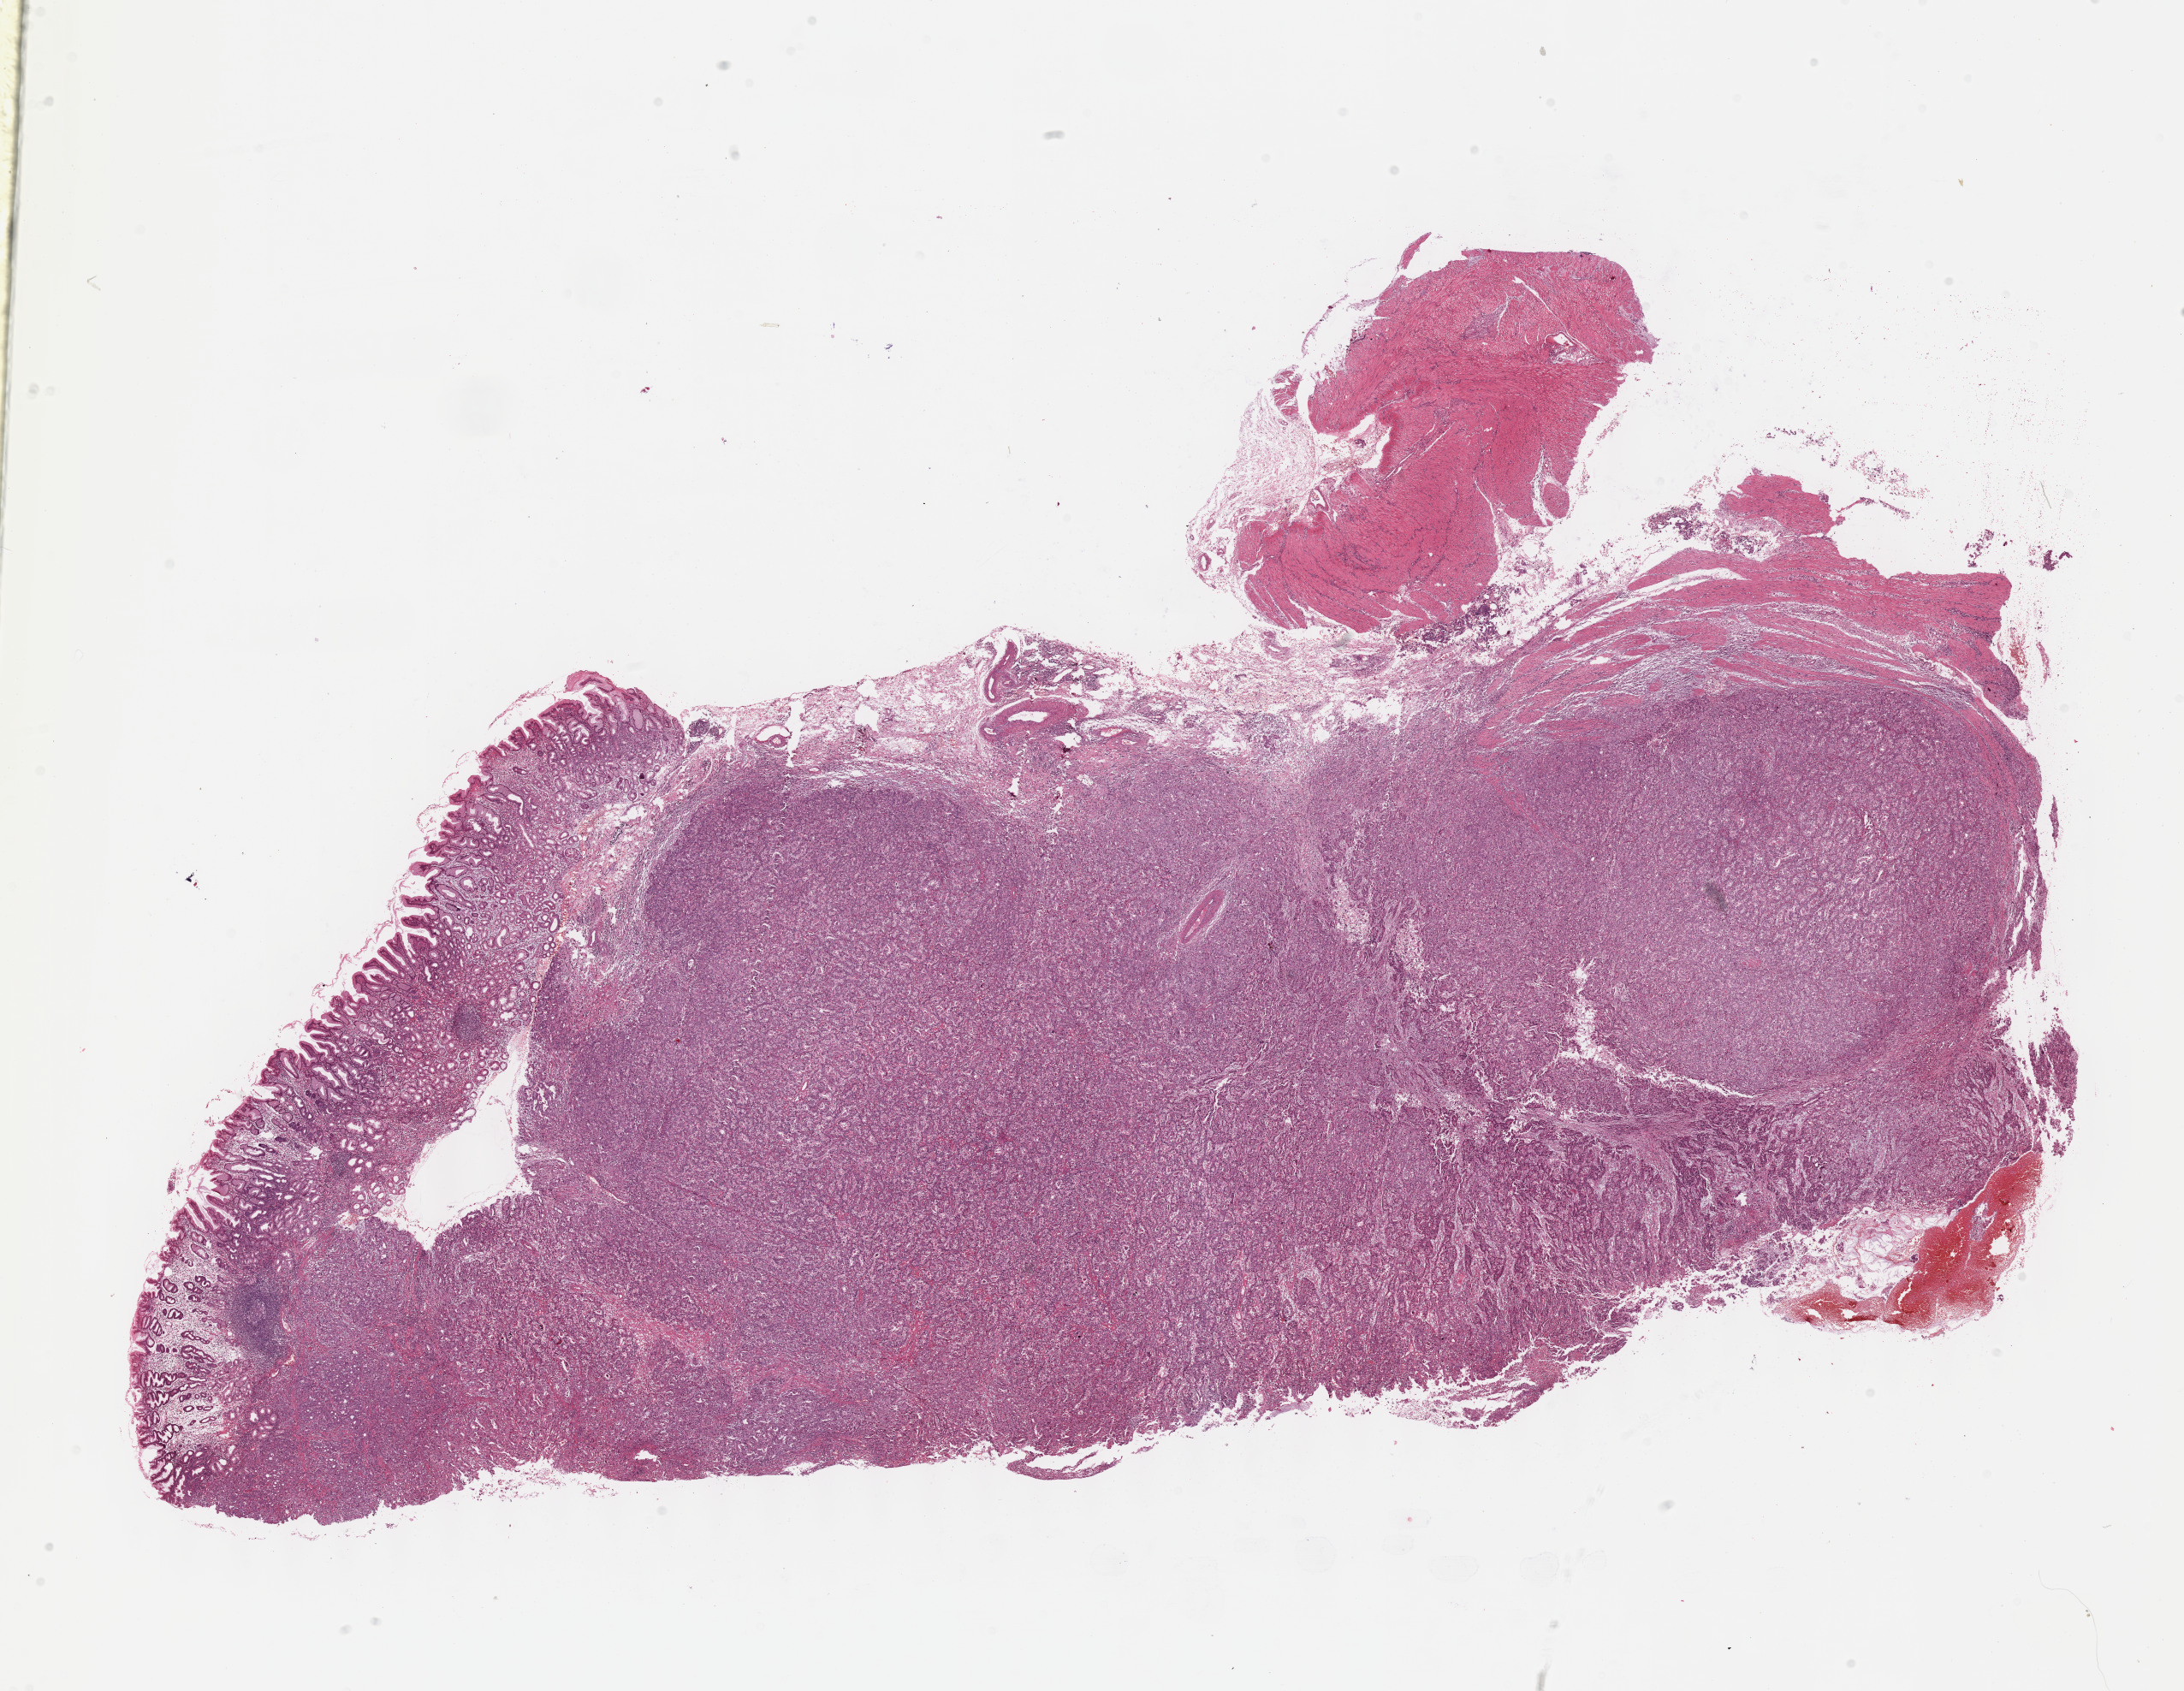
H&E whole-slide image — whole scanned area (about 20.6 x 16.0 mm) shown as a low-resolution overview, FFPE section, sample: primary tumour, stomach. Female, age 73 years at initial diagnosis. Histologic grade: G3 (poorly differentiated).
TNM: T3 N1 M0. Diagnosis: Adenocarcinoma, intestinal type (fundus of stomach). AJCC pathologic stage: IIIA.